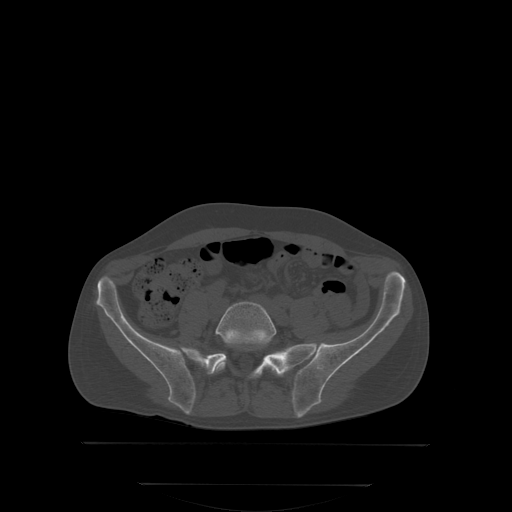
CT including the spine, one axial slice. Bone window (W 1800 / L 400 HU). 2.5 mm slice thickness. 512 × 512 image matrix, field of view 500 × 500 mm. Male patient, age 58 years. From the clinical record (not read from this slice): primary cancer: prostate.
Structures marked on this image (semi-automatically segmented with operator editing):
- L5 vertebra: box from (x=215, y=301) to (x=277, y=374) px